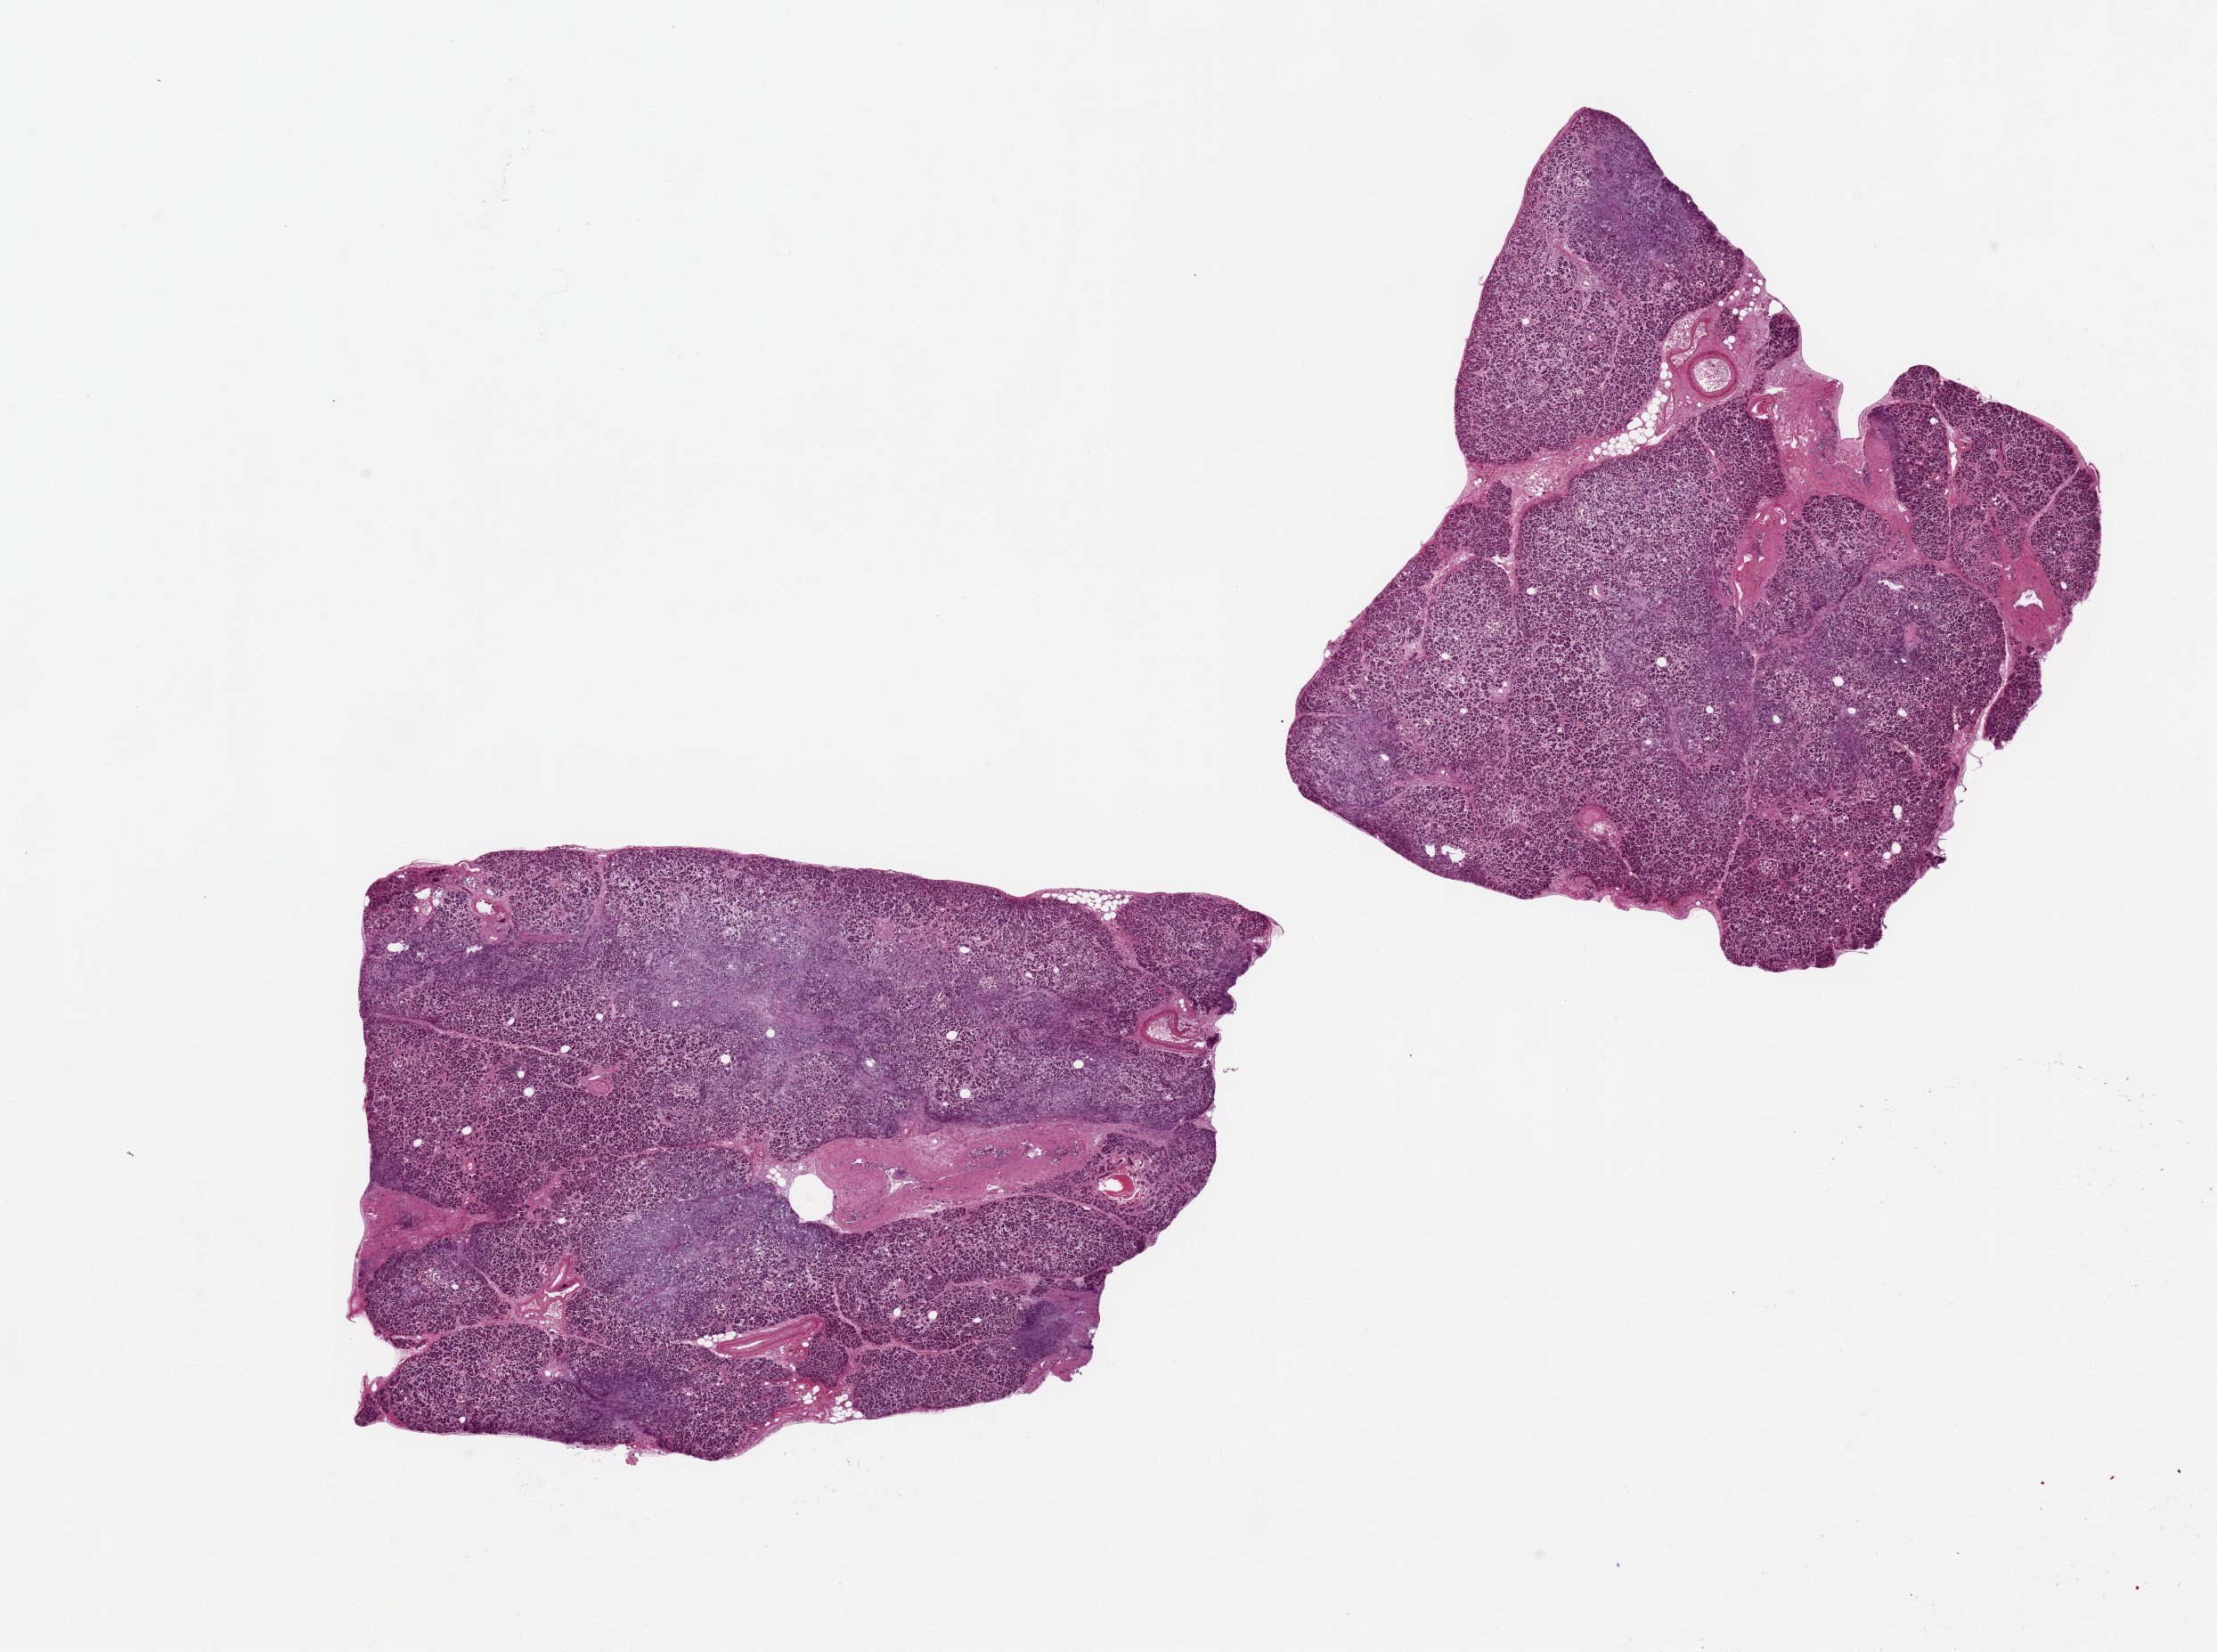
H&E whole-slide image, whole scanned area (about 19.7 x 14.7 mm, acquisition: 20x scan) shown as a low-resolution overview. PAXgene-fixed paraffin-embedded (PFPE) section. Section of pancreas (target tissue). Tissue donor sample. Donor: female.
Reviewer comment on this tissue sample: 2 pieces, 7x5 & 6x5 mm; extensive parenchymal autolysis focally severe.